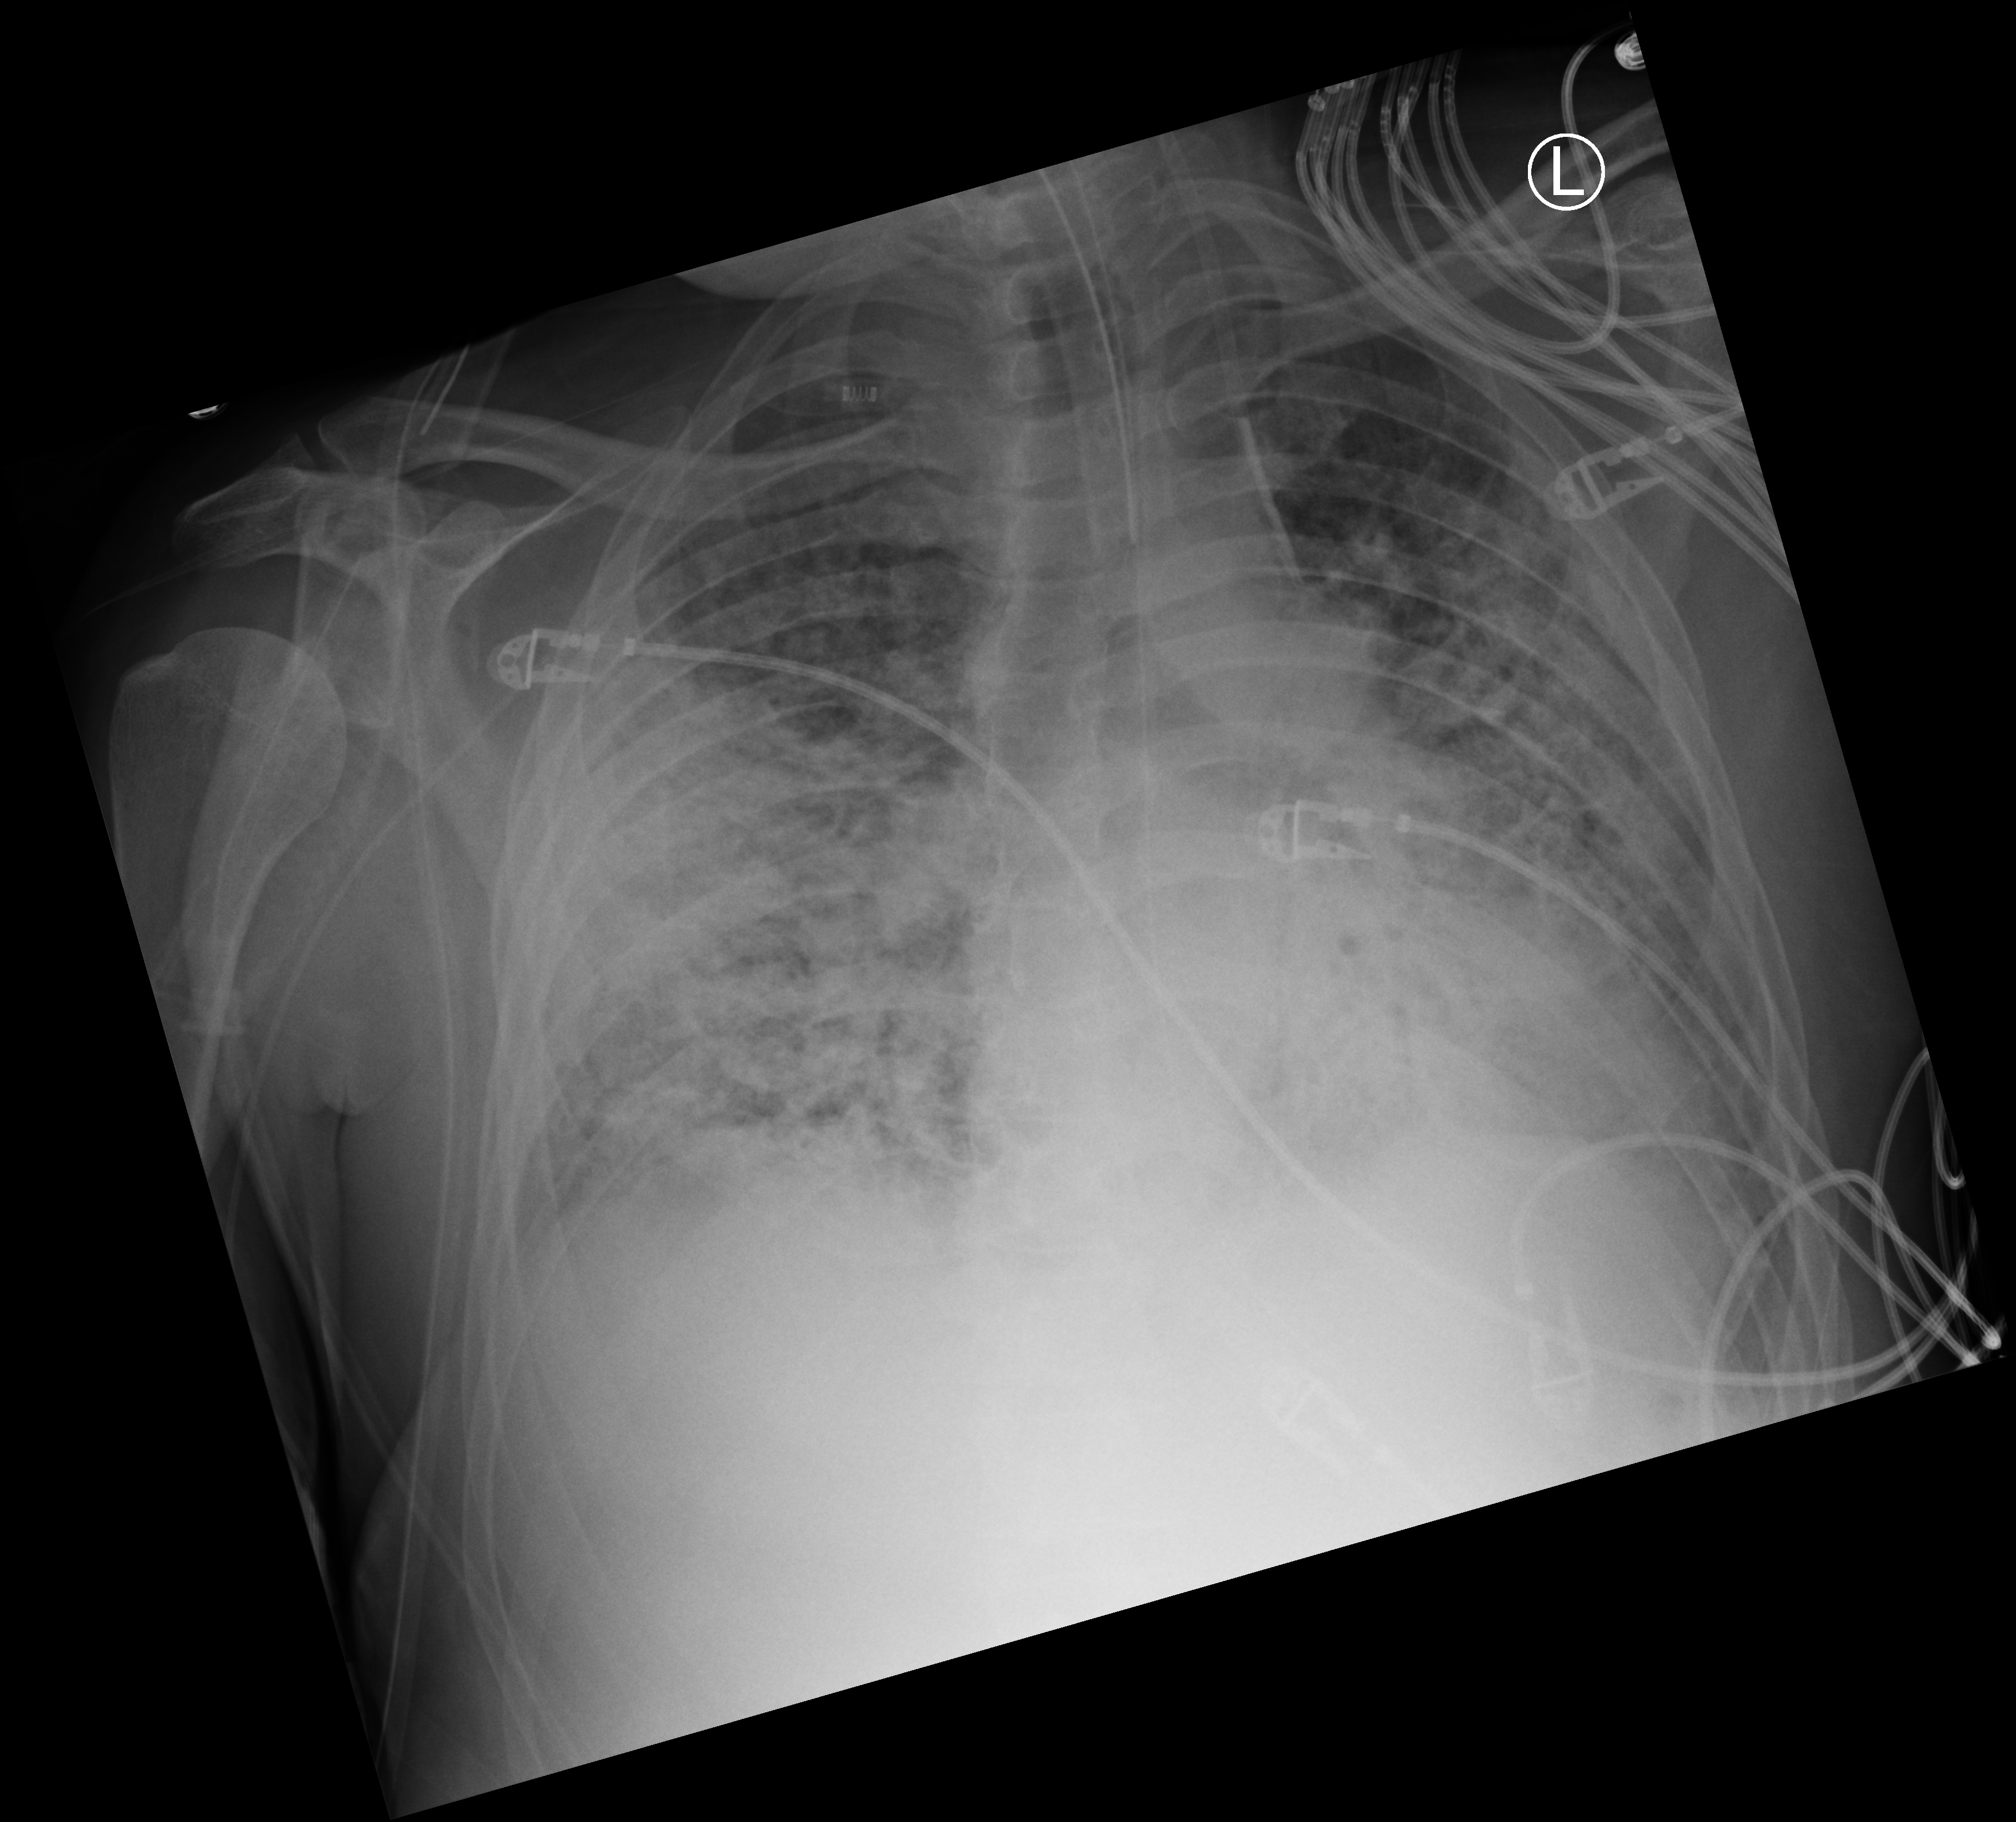
Chest X-ray (portable). Patient hospitalised with COVID-19; male, aged 18–59 years.
Hospital-stay facts (about this admission, not read from this image; timing relative to this image not recorded): admitted to intensive care during this hospital stay: yes; length of hospital stay: 75 days; smoking status (admission record): never.